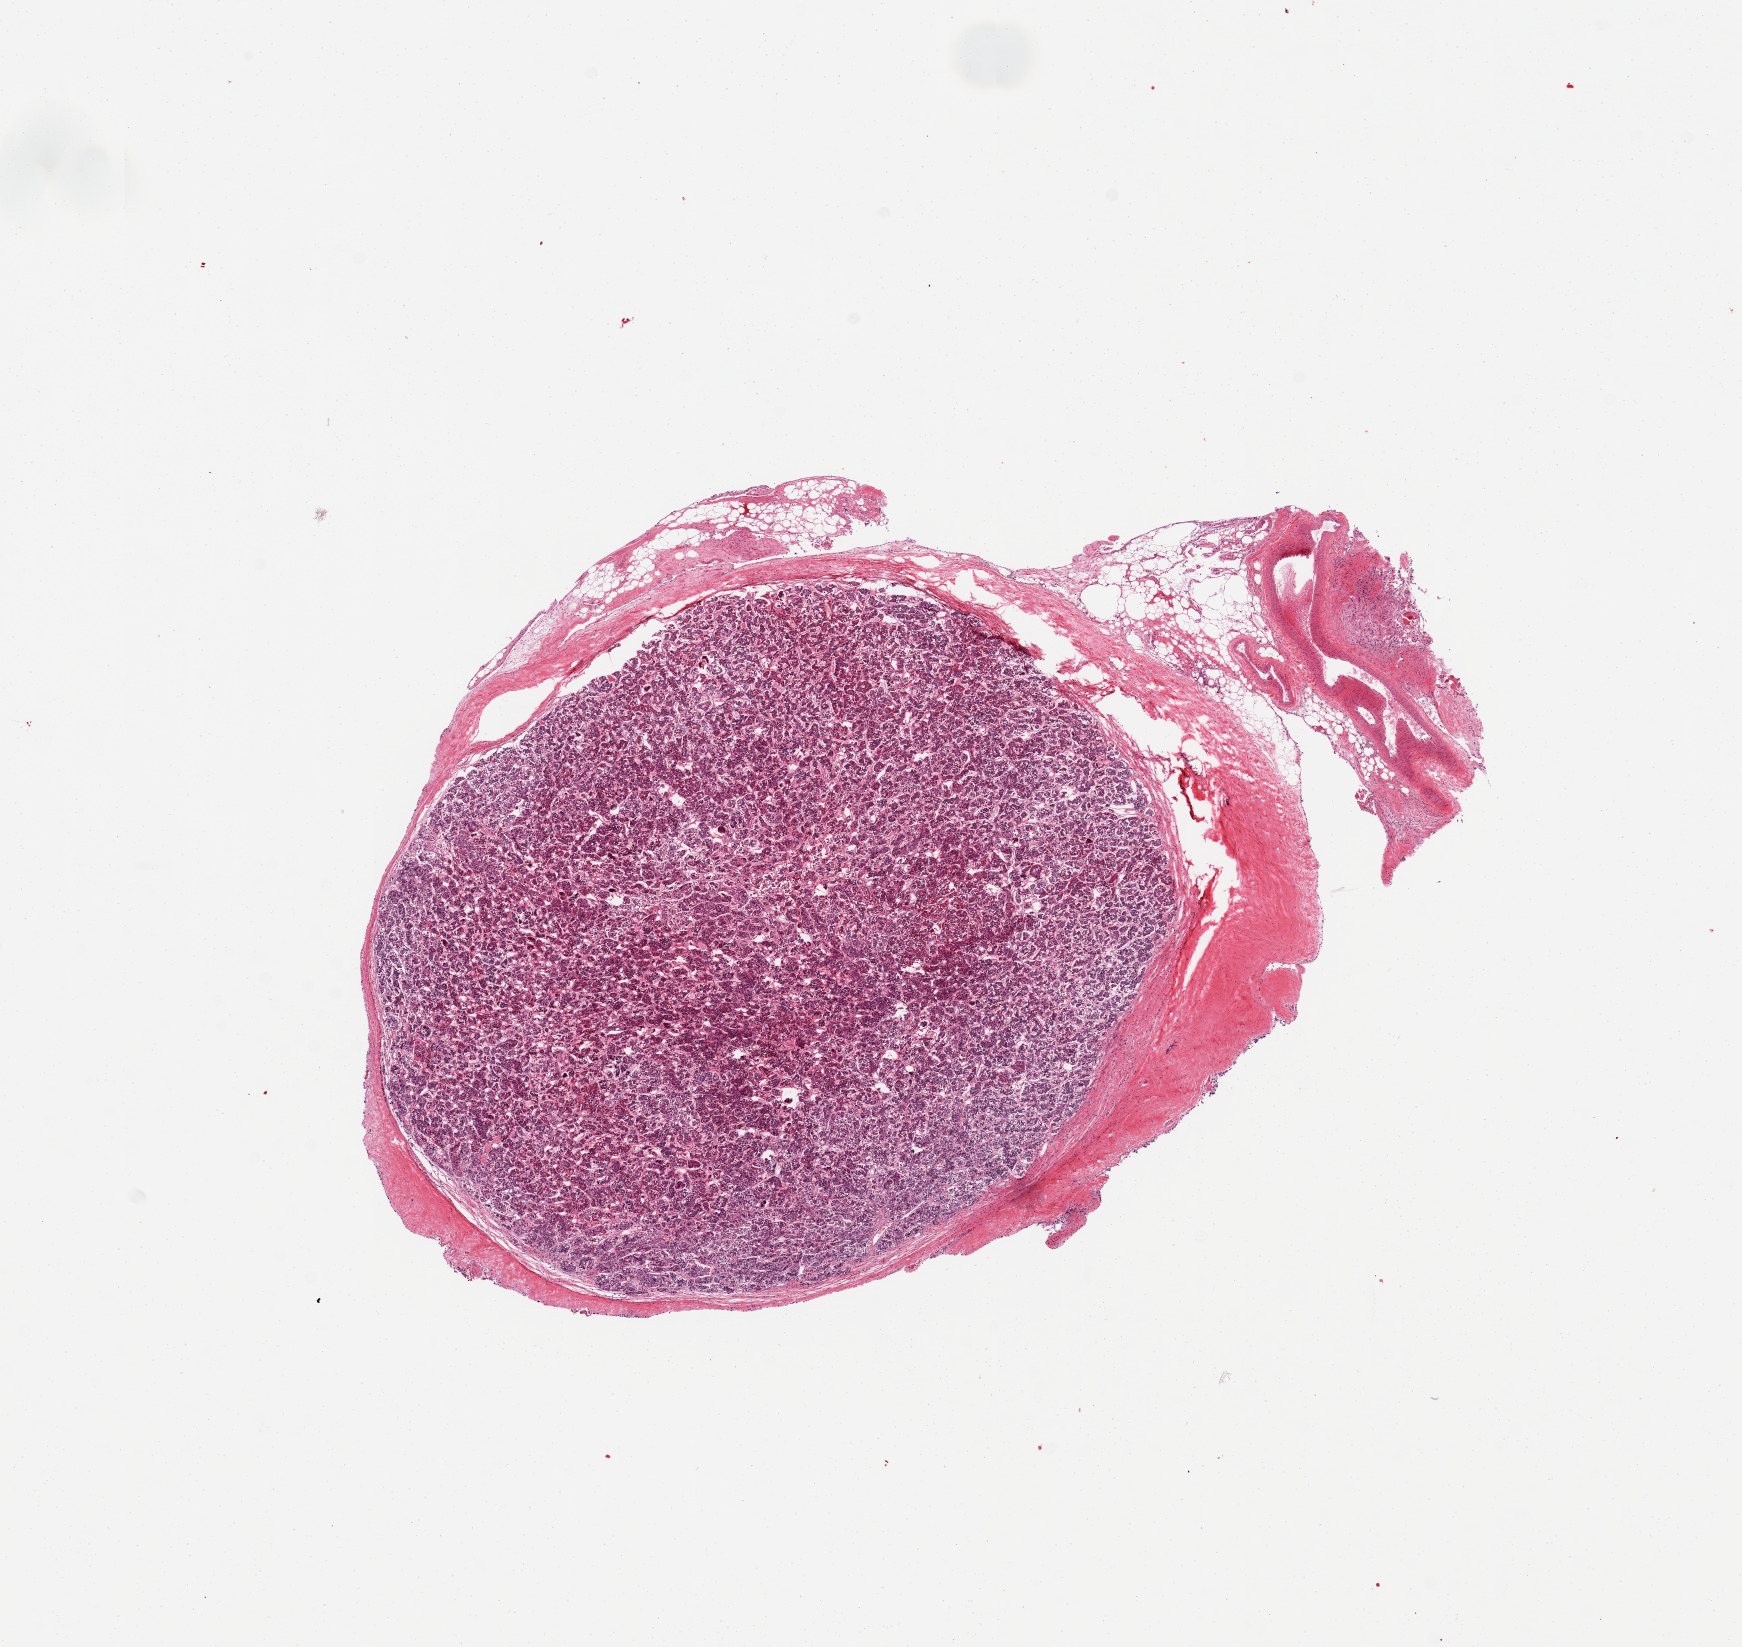
Whole-slide image, hematoxylin and eosin (H&E) stain — a low-resolution overview of the entire scanned area, about 13.8 x 13.0 mm; PAXgene-fixed, paraffin-embedded tissue; section of pituitary (target tissue); donor tissue sample. Donor: male.
Review note (as recorded): 1 piece; up to 2 mm adherent stroma and vessels.